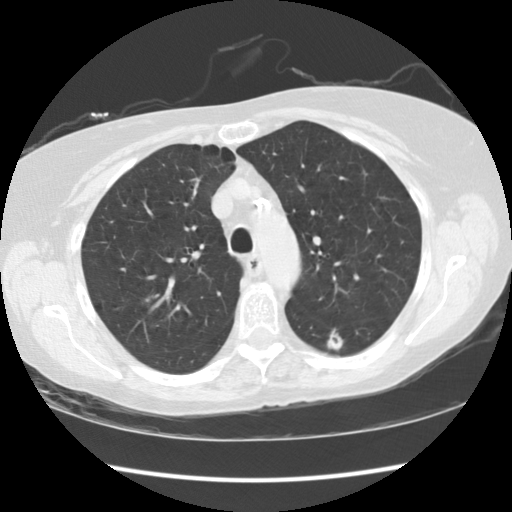
Axial slice from a low-dose chest CT screening exam; third screening round (two years after baseline); lung window (W 1500 / L -600 HU); 2.5 mm slice thickness; standard (soft-tissue) reconstruction kernel (STANDARD); 120 kVp; slice 33 of 119 in the series. Female participant, aged 63 years at enrolment. Current smoker at enrolment.
Expert reader's lesion annotation, bounding box (x1, y1, x2, y2) in pixels: (311, 319, 357, 358). The screening reader recorded 4 non-calcified nodules or masses ≥4 mm on this exam (left lower lobe, right upper lobe, left upper lobe, left lower lobe); which of them this box marks is not recorded. Official screen result: positive, other. Participant outcome: lung cancer diagnosed 60 days after this screen — squamous cell carcinoma, NOS, left lower lobe, moderately differentiated (G2), stage IB (AJCC 6th edition), 15 mm at pathology.